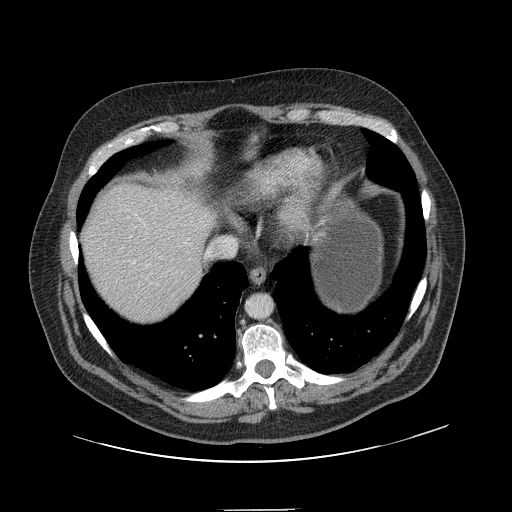
Contrast-enhanced abdominal CT, one axial slice. Slice 131 of 154 in the series (ordered by position). 120 kVp. Intravenous contrast given. Soft-tissue window (W 400 / L 40 HU). 2.5 mm slice thickness. 512 × 512 image matrix, field of view 451 × 451 mm. Male patient, age 61 years. Case-level facts recorded for this patient, not image findings: diagnosis: colorectal cancer liver metastases, imaged before liver resection; multiple liver metastases: yes; largest metastasis: 2.6 cm.
Outlined on this slice (manually delineated by an expert):
- hepatic veins: box from (x=160, y=257) to (x=162, y=259) px
- liver: (x=83, y=186)–(x=214, y=320)
- planned liver remnant (the part of the liver to remain after resection): (x=83, y=185)–(x=214, y=320)
- portal vein (with intrahepatic branches): (x=127, y=216)–(x=149, y=278)